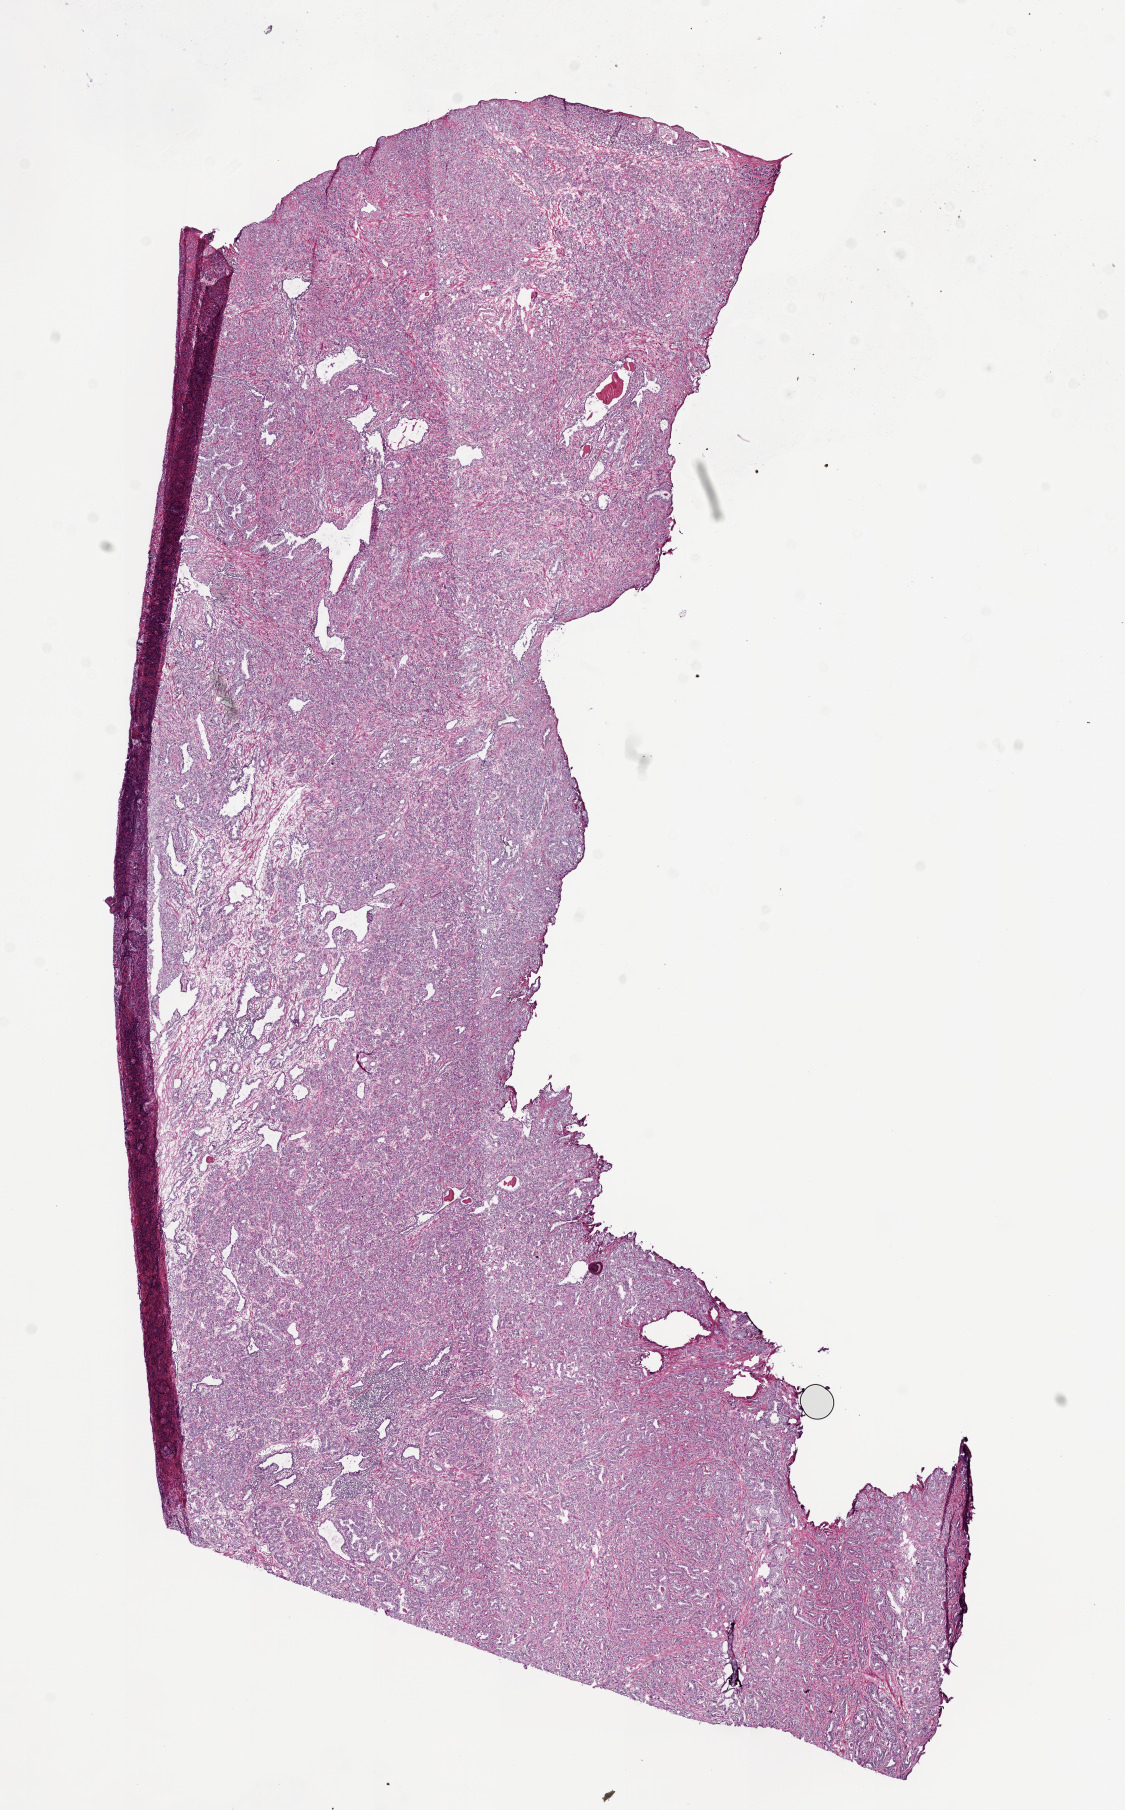
Digitized Hematoxylin and eosin (H&E) stained tissue section (whole slide), shown as a low-resolution overview of the whole scanned area (about 9.0 x 14.5 mm), frozen section from the bottom of the tissue portion, sample: primary tumour, prostate. Patient: male, age at initial diagnosis 50 years. Gleason score: 8 (5+3). Composition of this section per pathologist review: tumour cells 80%, tumour nuclei 85%, normal cells 5%, stromal cells 10%, necrosis 0%. Infiltration values recorded for this section: lymphocyte infiltration 0%, monocyte infiltration 0%, neutrophil infiltration 0%.
Lymph nodes positive (case pathology): 0 of 21 examined. Laterality: bilateral. Pathologic diagnosis: Acinar cell carcinoma (prostate gland).